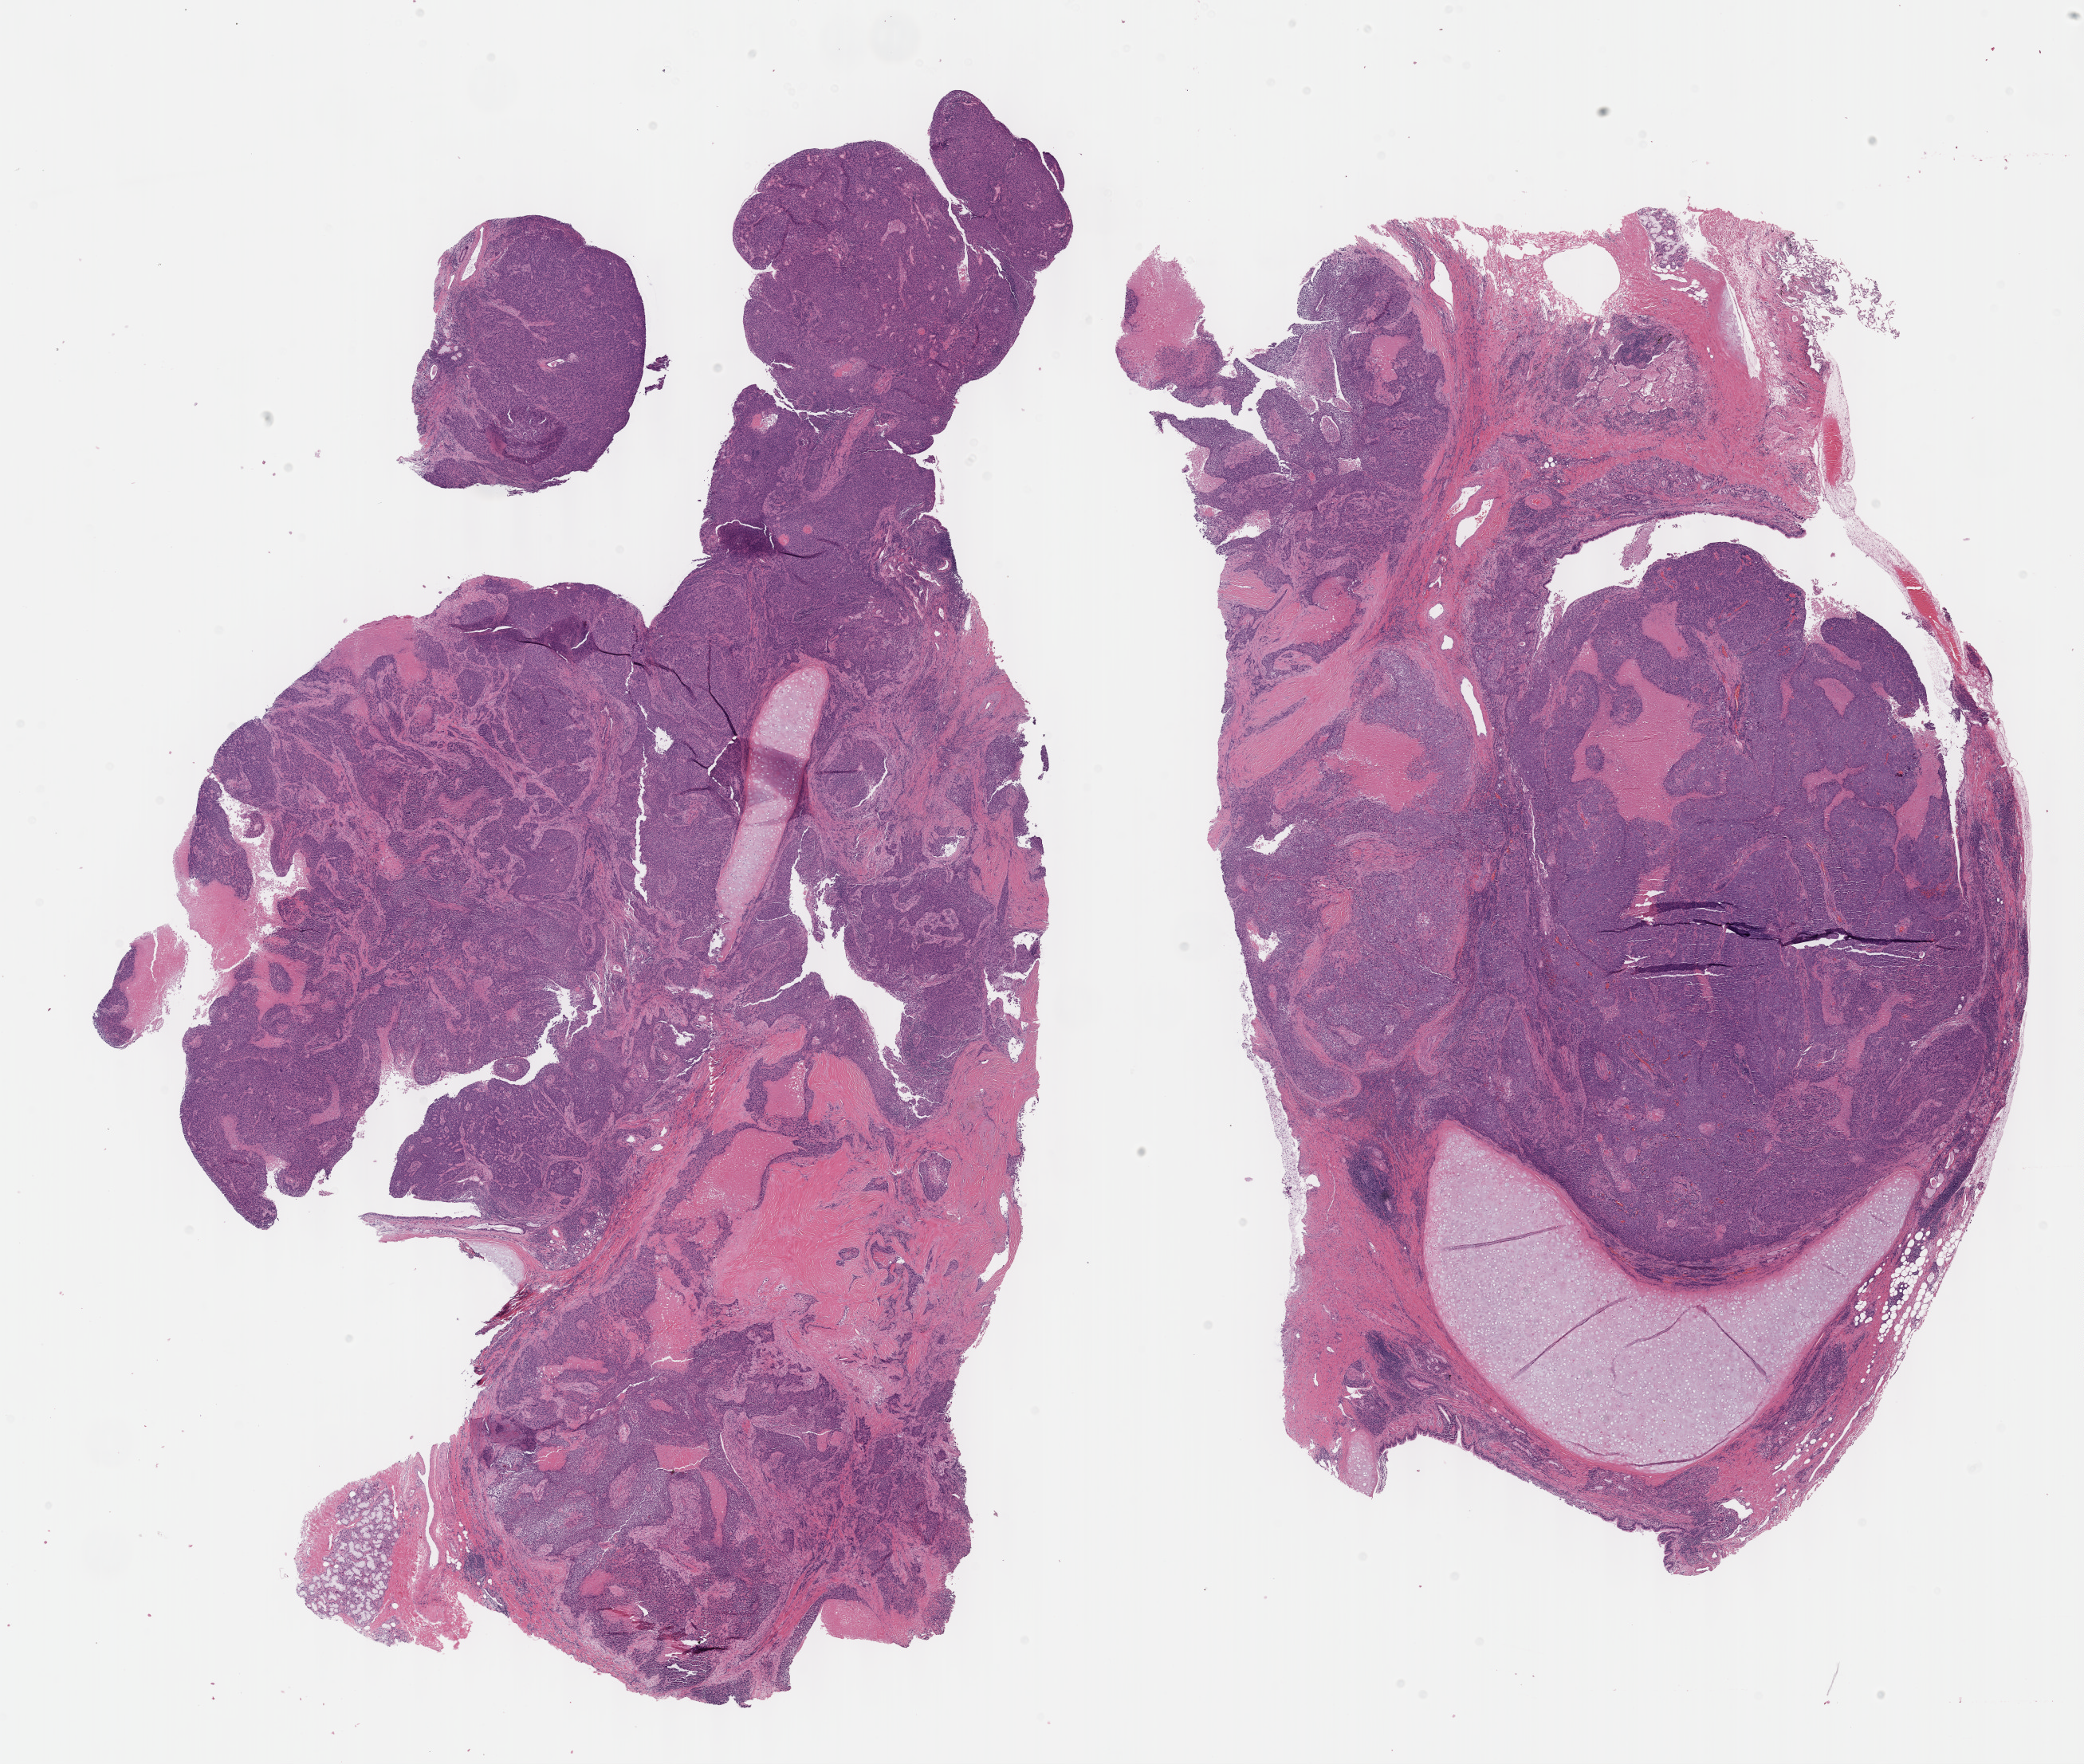
Digitized H&E tissue section (whole slide) — shown as a low-resolution overview of the whole scanned area (about 21.1 x 17.9 mm), formalin-fixed paraffin-embedded (FFPE) diagnostic section, primary tumour sample from the lung. Male, age 64 years at initial diagnosis.
- histologic diagnosis: Squamous cell carcinoma, NOS (upper lobe, lung)
- AJCC pathologic stage: IA
- laterality: left